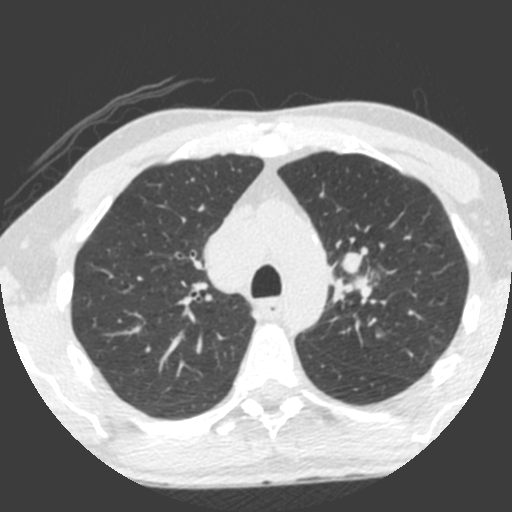
Low-dose screening chest CT, one axial slice; slice 156 of 212 in the series (ordered by position); lung window (W 1500 / L -600 HU); 2 mm slice thickness; 512 × 512 image matrix, field of view 315 × 315 mm.
Annotated regions visible in this slice (outlined manually by an expert reader):
- lesion 1 (tumor, upper lobe of left lung): bounding box [x1, y1, x2, y2] px = [340, 246, 368, 275]